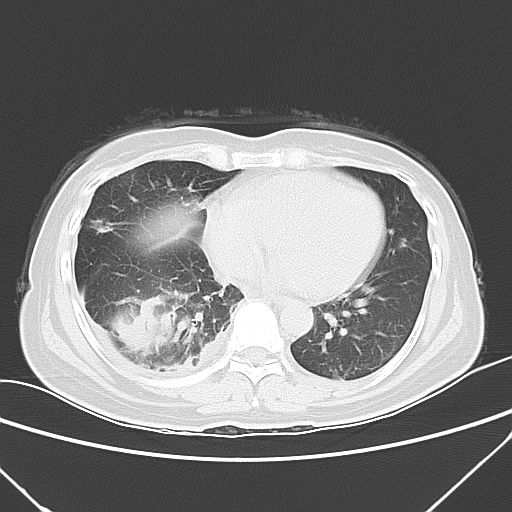
Chest CT, one axial slice. Position 17 of 53 along the scan axis. Lung window (W 1500 / L -600 HU). 512 × 512 image matrix, field of view 337 × 337 mm. Patient: female, 42 years. Case-level facts recorded for this patient, not image findings: clinical TNM (as recorded): T3 N0 M1c.
Annotated regions visible in this slice (rectangle marked by the reading radiologist):
- lung tumour (recorded histology: adenocarcinoma): bounding box <105,299,180,352> (left, top, right, bottom; pixels)